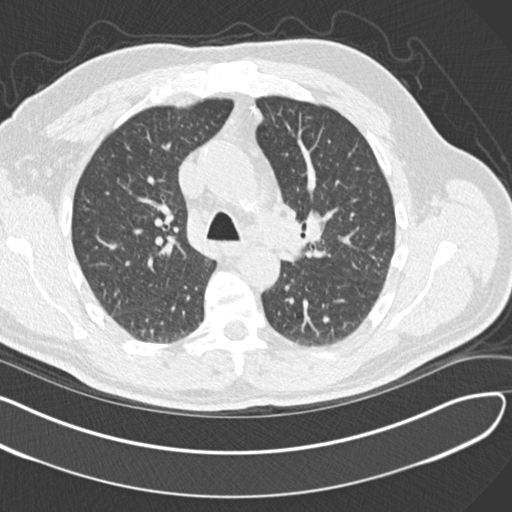
Axial slice from a low-dose chest CT screening exam, second screening round (one year after baseline), lung window (W 1500 / L -600 HU), standard (soft-tissue) reconstruction kernel (B30f), 120 kVp, slice 50 of 164 in the series. Male, age 65 years at enrolment. Former smoker at enrolment.
- Expert reader's lesion annotation, bounding box [x1, y1, x2, y2] px = [288, 195, 350, 259].
- The screening reader recorded 4 non-calcified nodules or masses ≥4 mm on this exam (left upper lobe, left upper lobe, left lower lobe, right middle lobe); which of them this box marks is not recorded.
- Official screen result: positive, other.
- Later outcome: lung cancer diagnosed 577 days after this screen — acinar cell carcinoma, left upper lobe, stage IA (AJCC 6th edition), 25 mm at pathology.